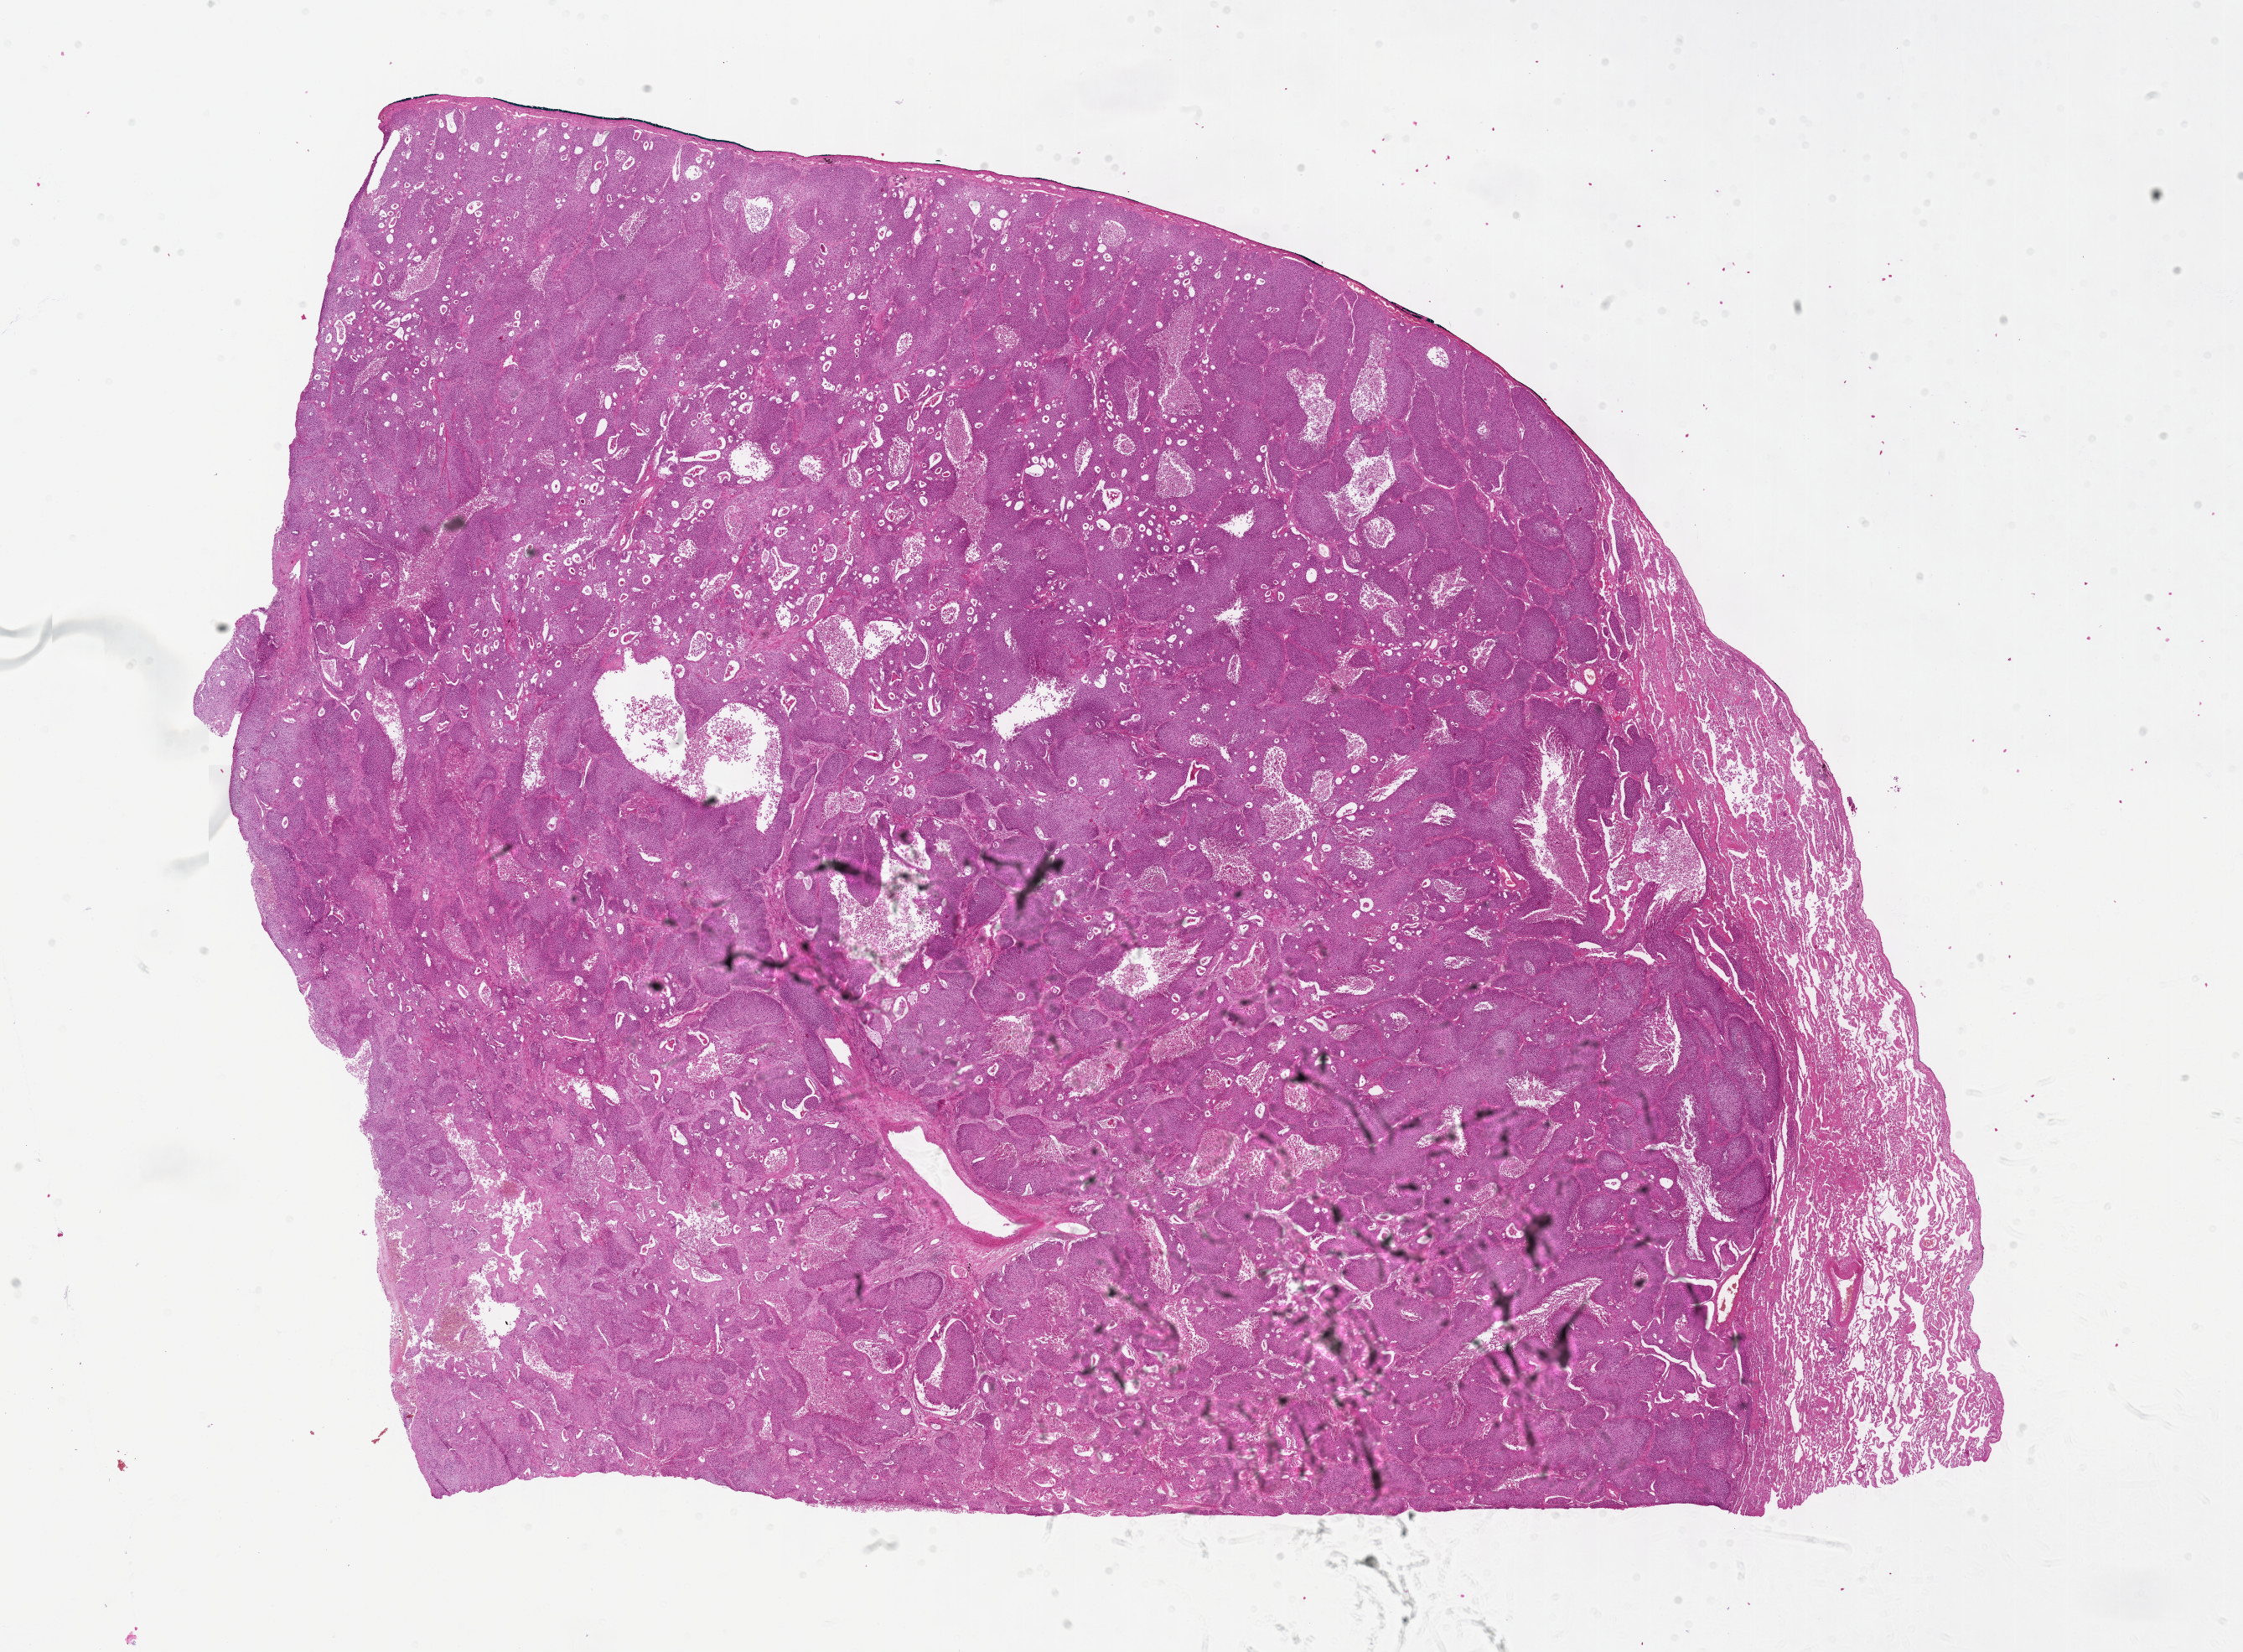
Whole-slide histology image, H&E, a low-resolution overview of the entire scanned area, about 21.6 x 15.9 mm (slide scanned at 40x); FFPE section; primary tumour sample from the lung. Male patient; age at initial diagnosis 74 years.
AJCC pathologic stage: IIIB (6th edition). Histologic diagnosis: Squamous cell carcinoma, keratinizing, NOS (lower lobe, lung). Laterality: left.